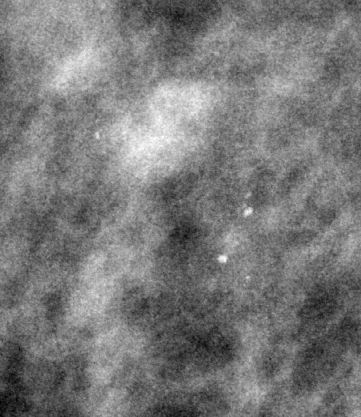
Crop from a digitized film mammogram around one marked abnormality, right breast, MLO view, BI-RADS breast density category 2 (scale 1–4).
Finding: calcifications, morphology pleomorphic, distribution clustered; BI-RADS assessment category 3; pathology result (as recorded, not read from the image): benign.